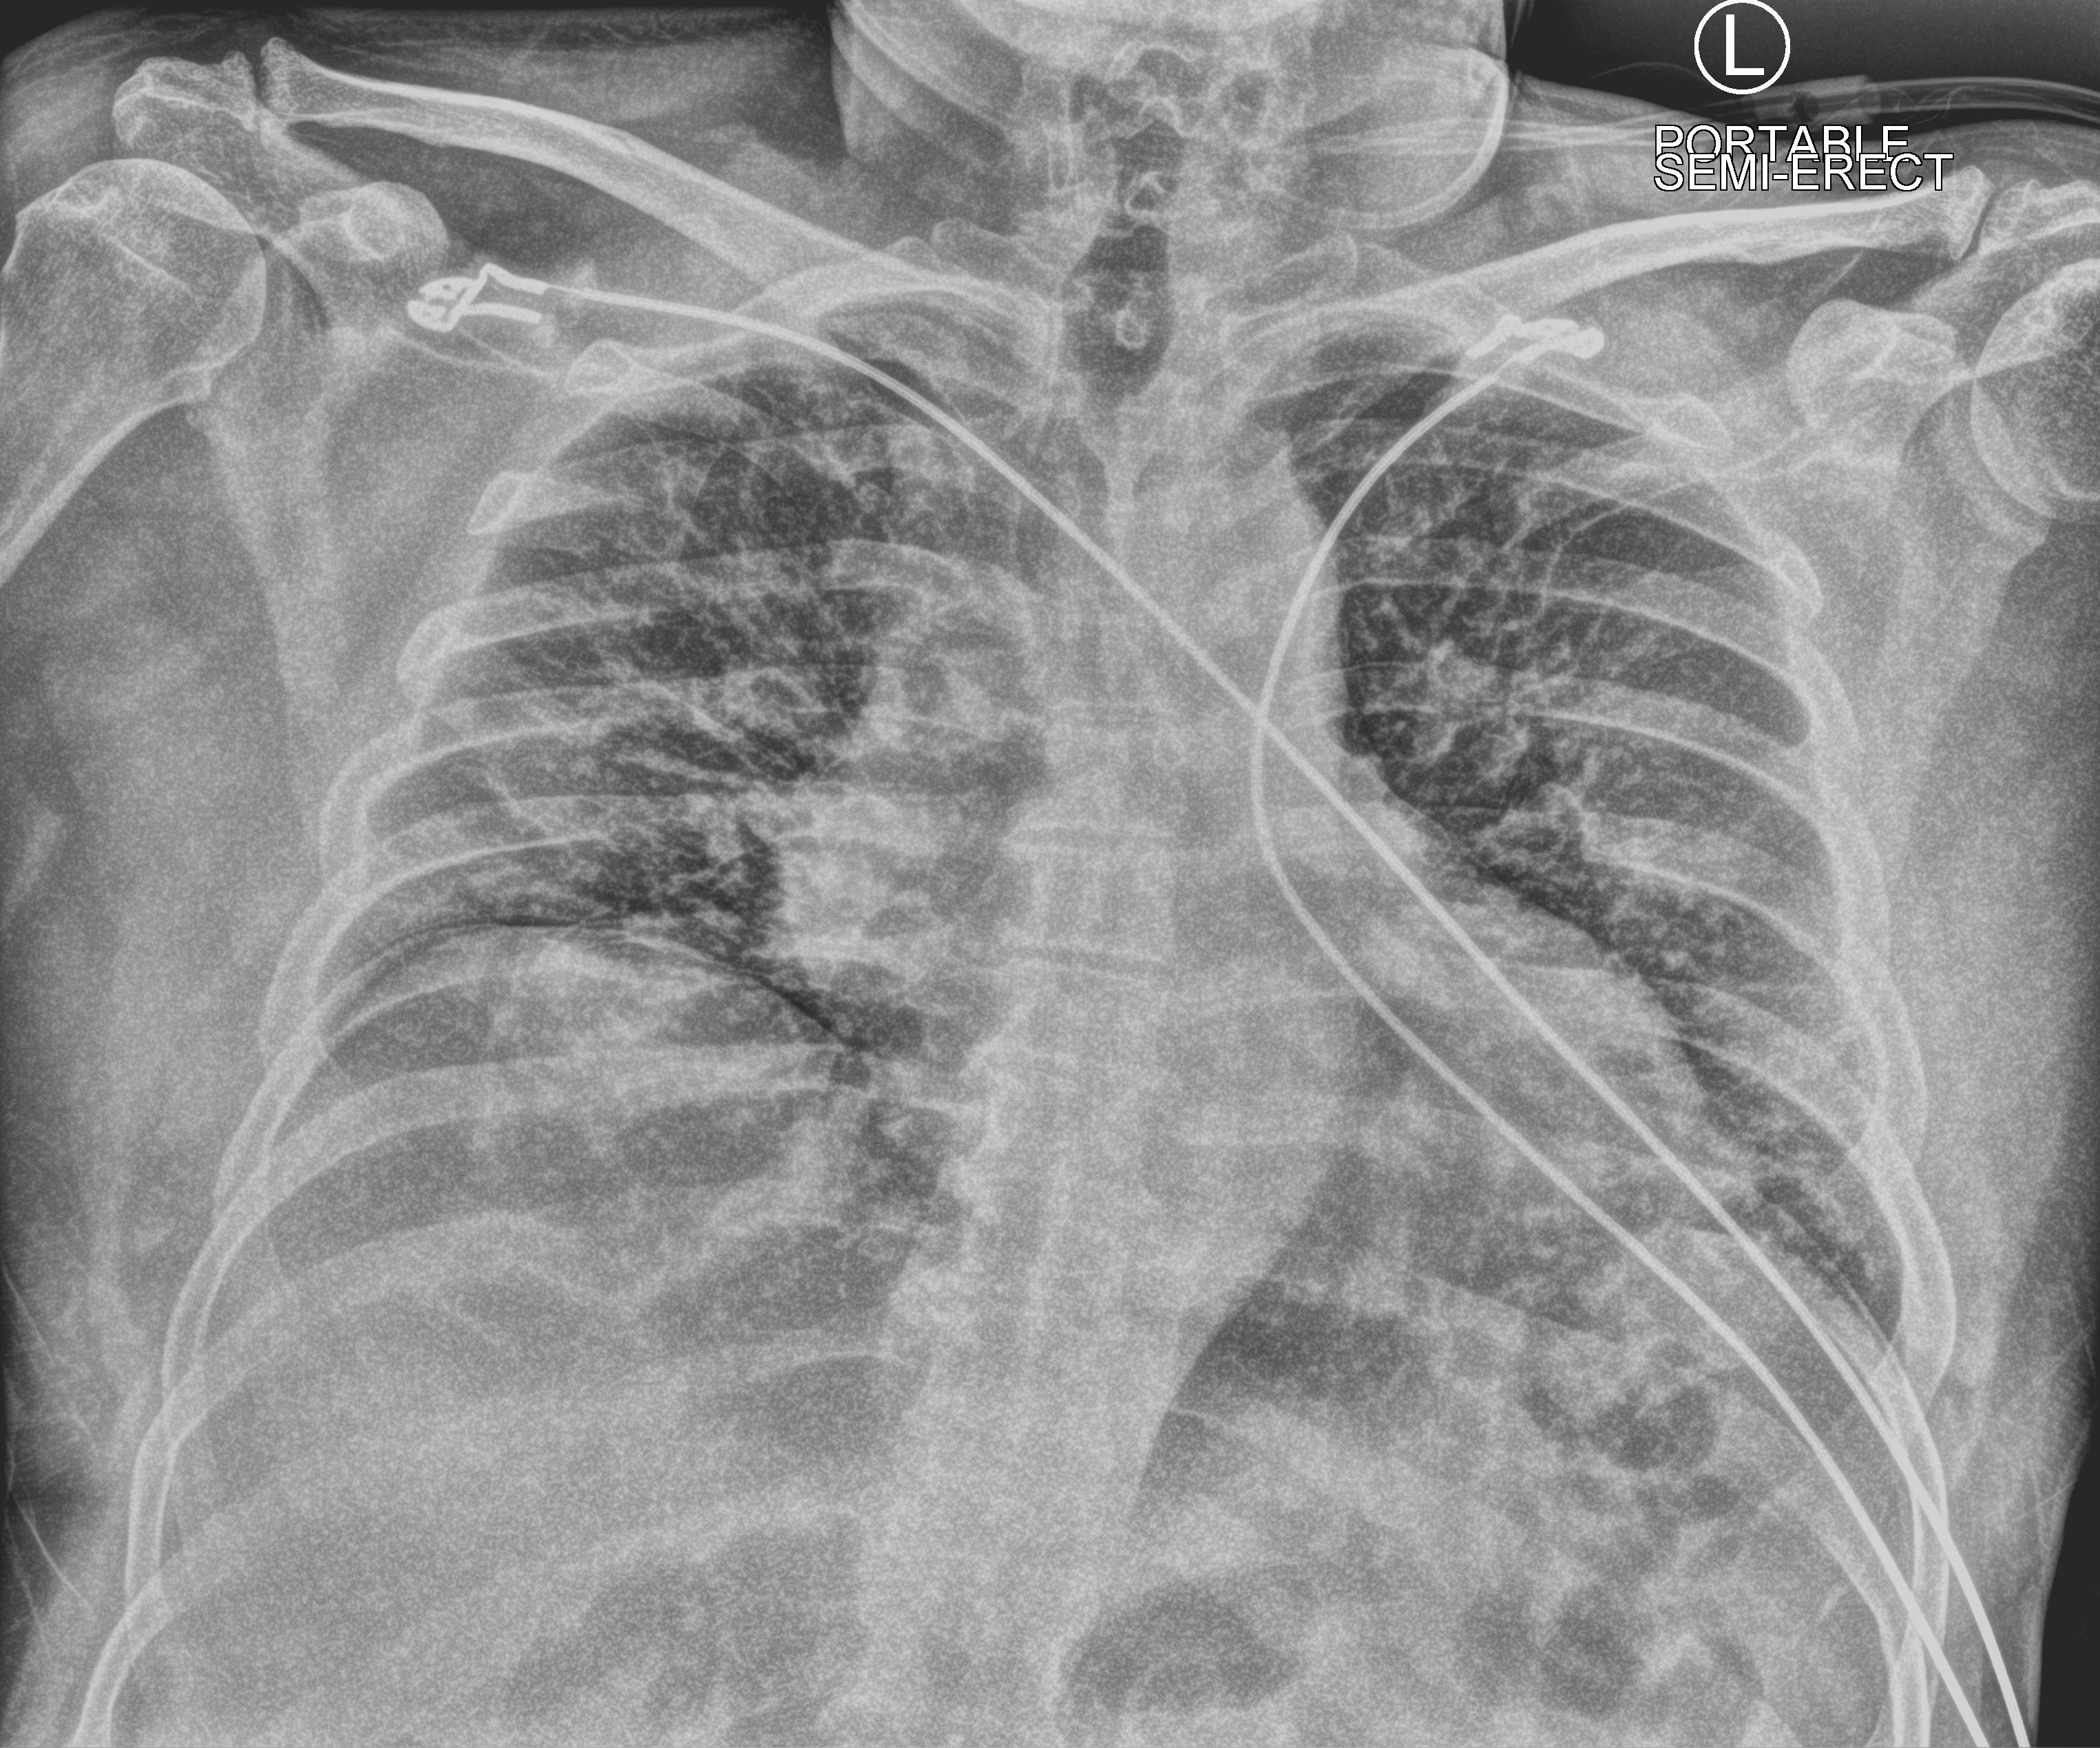
Portable chest radiograph, anteroposterior (AP) projection. Male patient hospitalised with COVID-19, age 18–59 years.
Admission-level facts for this patient (not findings on this image; timing relative to this image not recorded): chronic kidney disease (admission record): no; length of hospital stay: 18 days; hypertension (admission record): no.